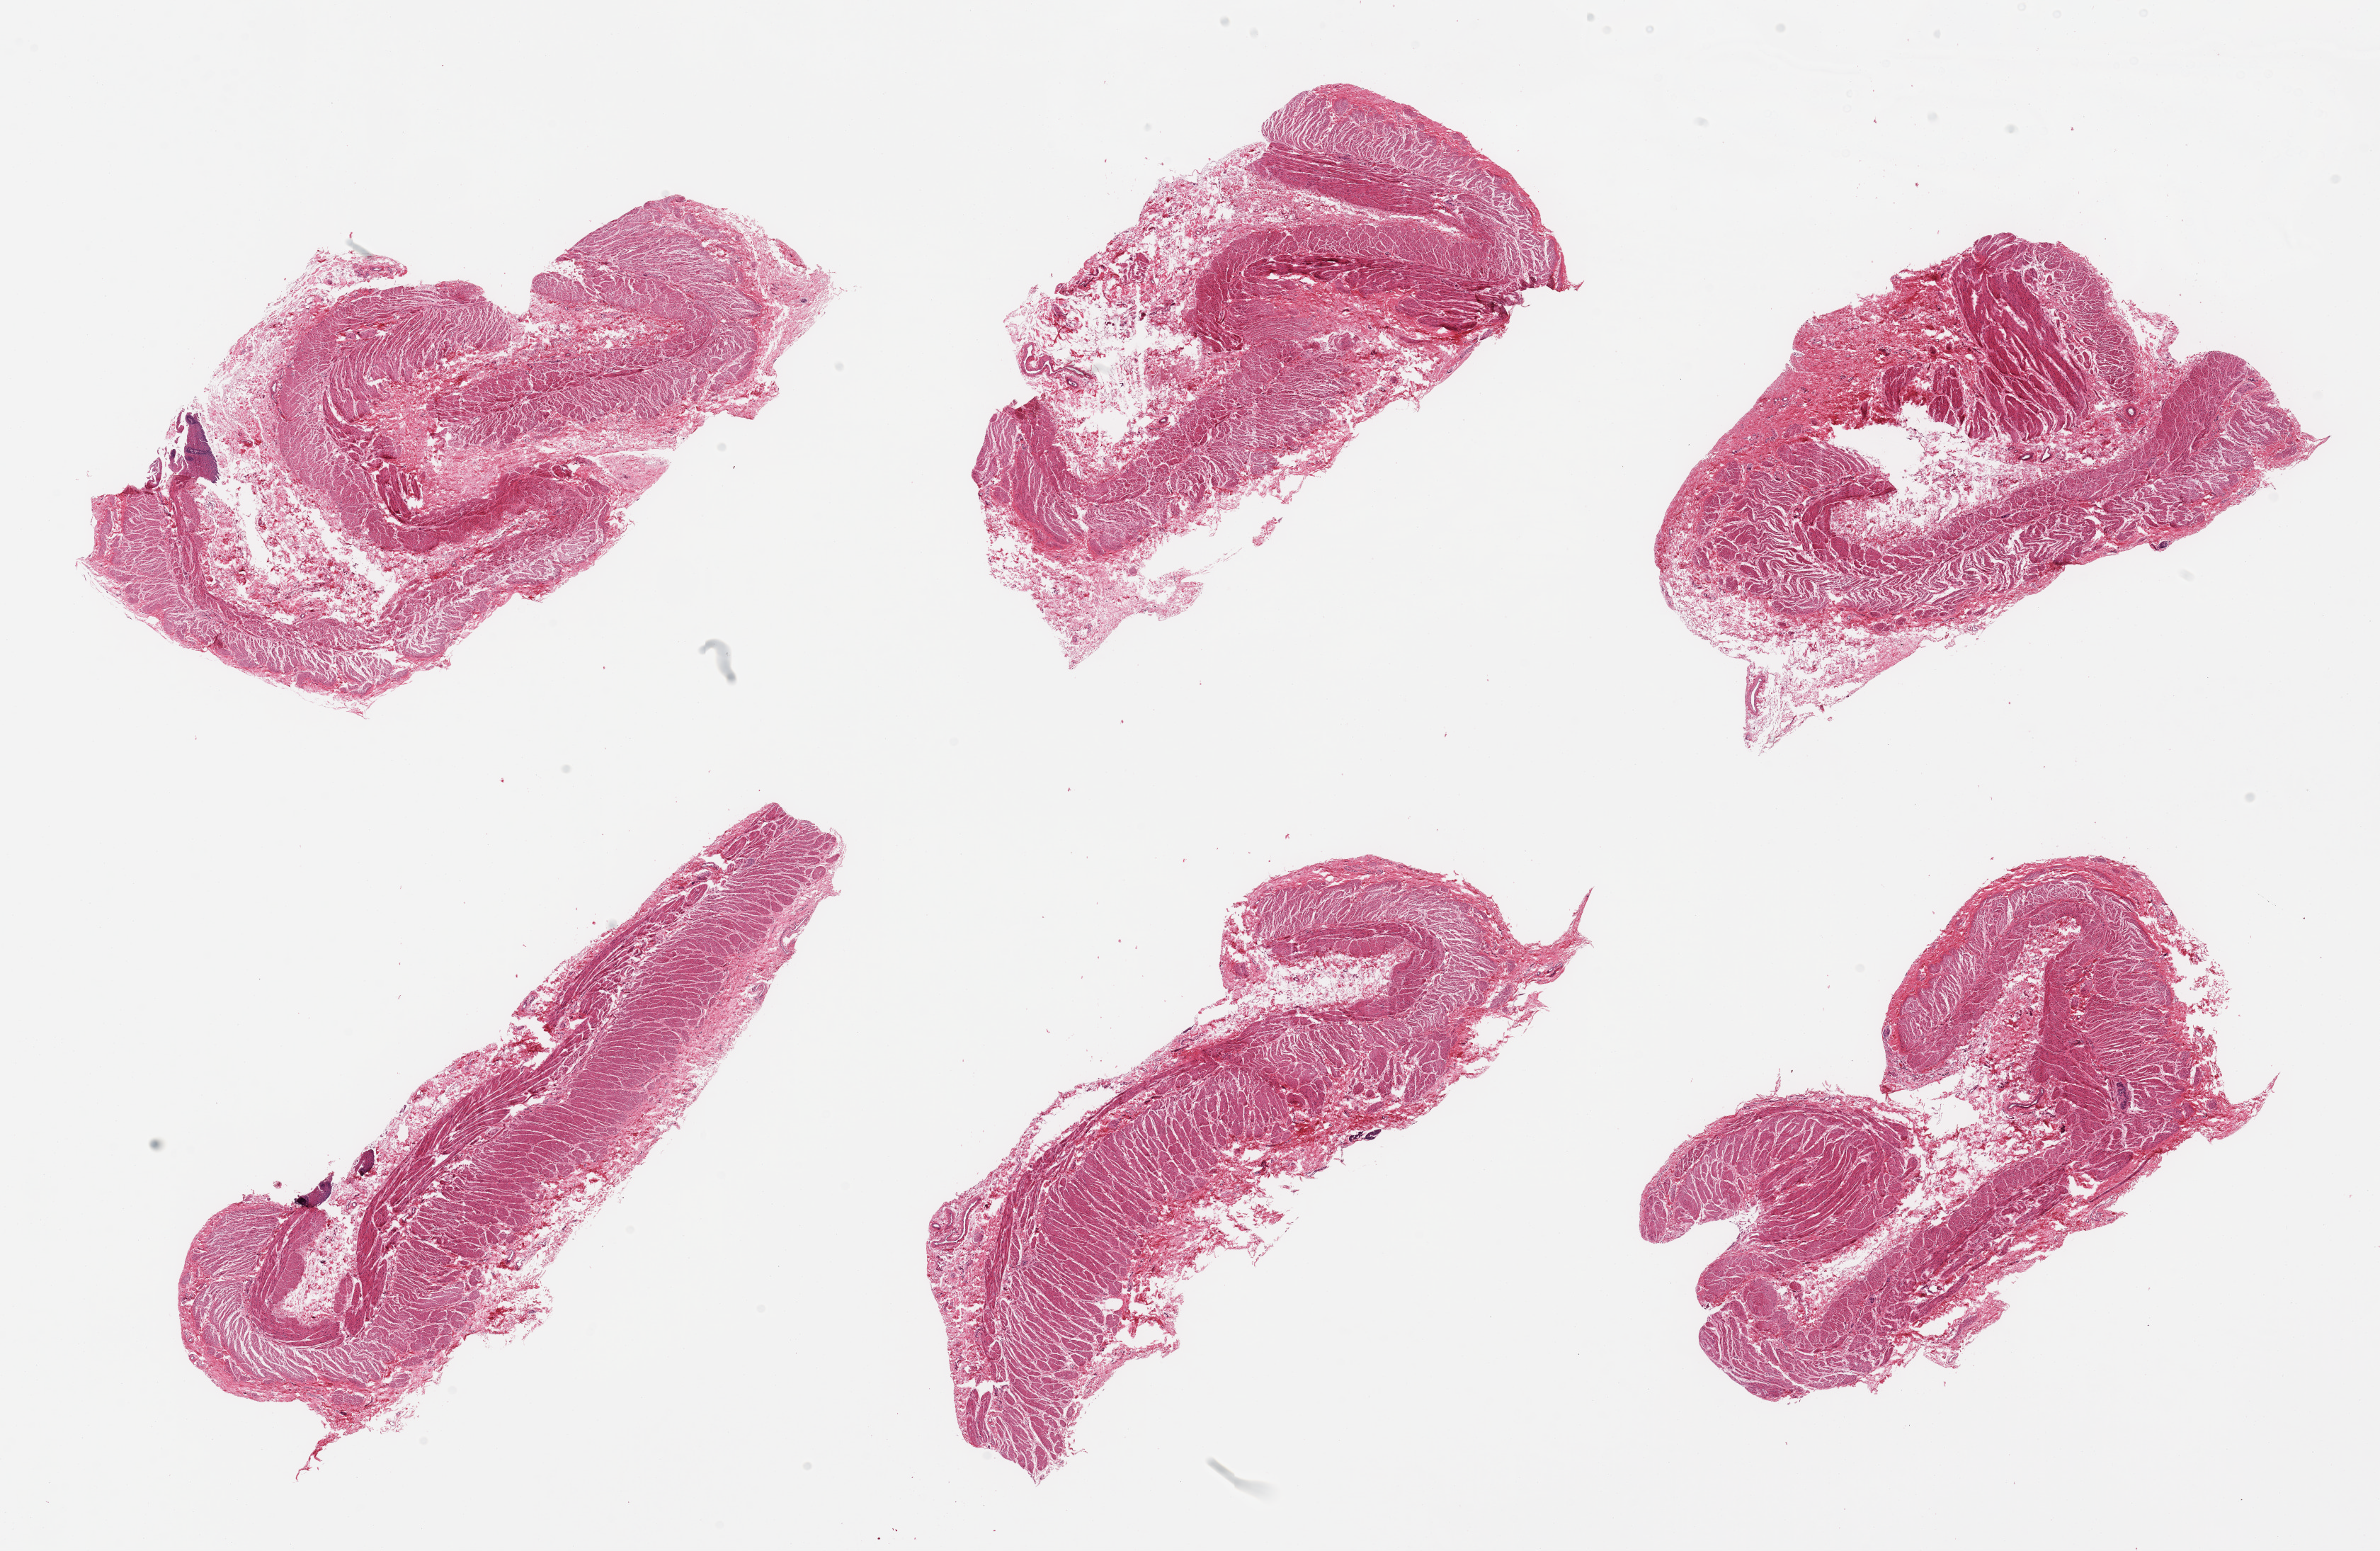
Digitized haematoxylin and eosin-stained section, low-resolution overview of the scanned area, about 26.6 x 17.3 mm (acquisition: 20x scan). PAXgene-fixed paraffin-embedded (PFPE) section. Sampled site (target tissue): gastroesophageal junction. Tissue donor sample. Donor: female.
Review note (as recorded): 6 pieces; muscularis, few detached fragments of squamous epithelium.